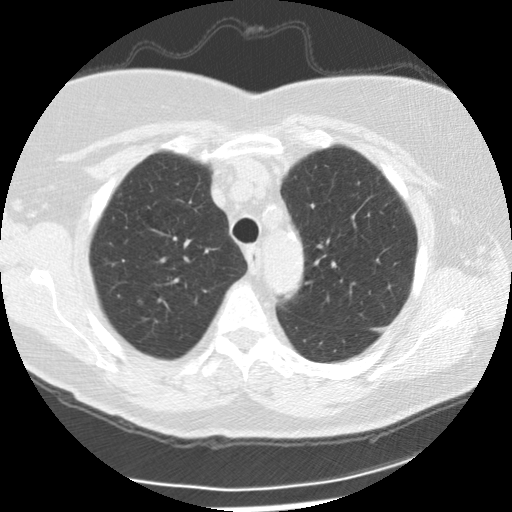
Axial slice from a low-dose chest CT screening exam; first (baseline) screen; lung window (W 1500 / L -600 HU); 2.5 mm slice thickness; standard (soft-tissue) reconstruction kernel (STANDARD); slice 50 of 225 in the series. Female, age 72 years at enrolment. Current smoker at enrolment.
Lesion marked by an expert reader, bounding box <124,295,149,315> (left, top, right, bottom; pixels). Screening reader's record for this exam: no non-calcified nodule ≥4 mm recorded. Official screen result: negative screen, minor abnormalities not suspicious for lung cancer. Participant outcome: lung cancer diagnosed 877 days after this screen — squamous cell carcinoma, NOS, right upper lobe, poorly differentiated (G3), stage IIIA (AJCC 6th edition), 22 mm at pathology.